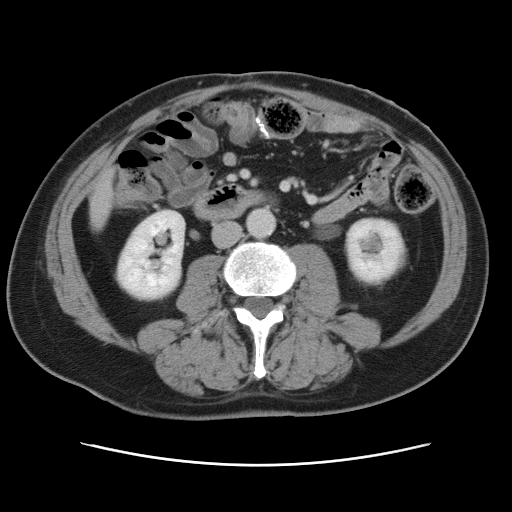
Contrast-enhanced abdominal CT, one axial slice; slice 13 of 80 in the series (ordered by position); 120 kVp; intravenous contrast given; soft-tissue window (W 400 / L 40 HU); 512 × 512 image matrix. Male patient, age 69 years. Case-level facts recorded for this patient, not image findings: diagnosis: colorectal cancer liver metastases, imaged before liver resection; multiple liver metastases: no; largest metastasis: 5 cm.
Outlined on this slice (expert manual segmentation):
- liver: bounding box [x1, y1, x2, y2] px = [90, 175, 113, 225]